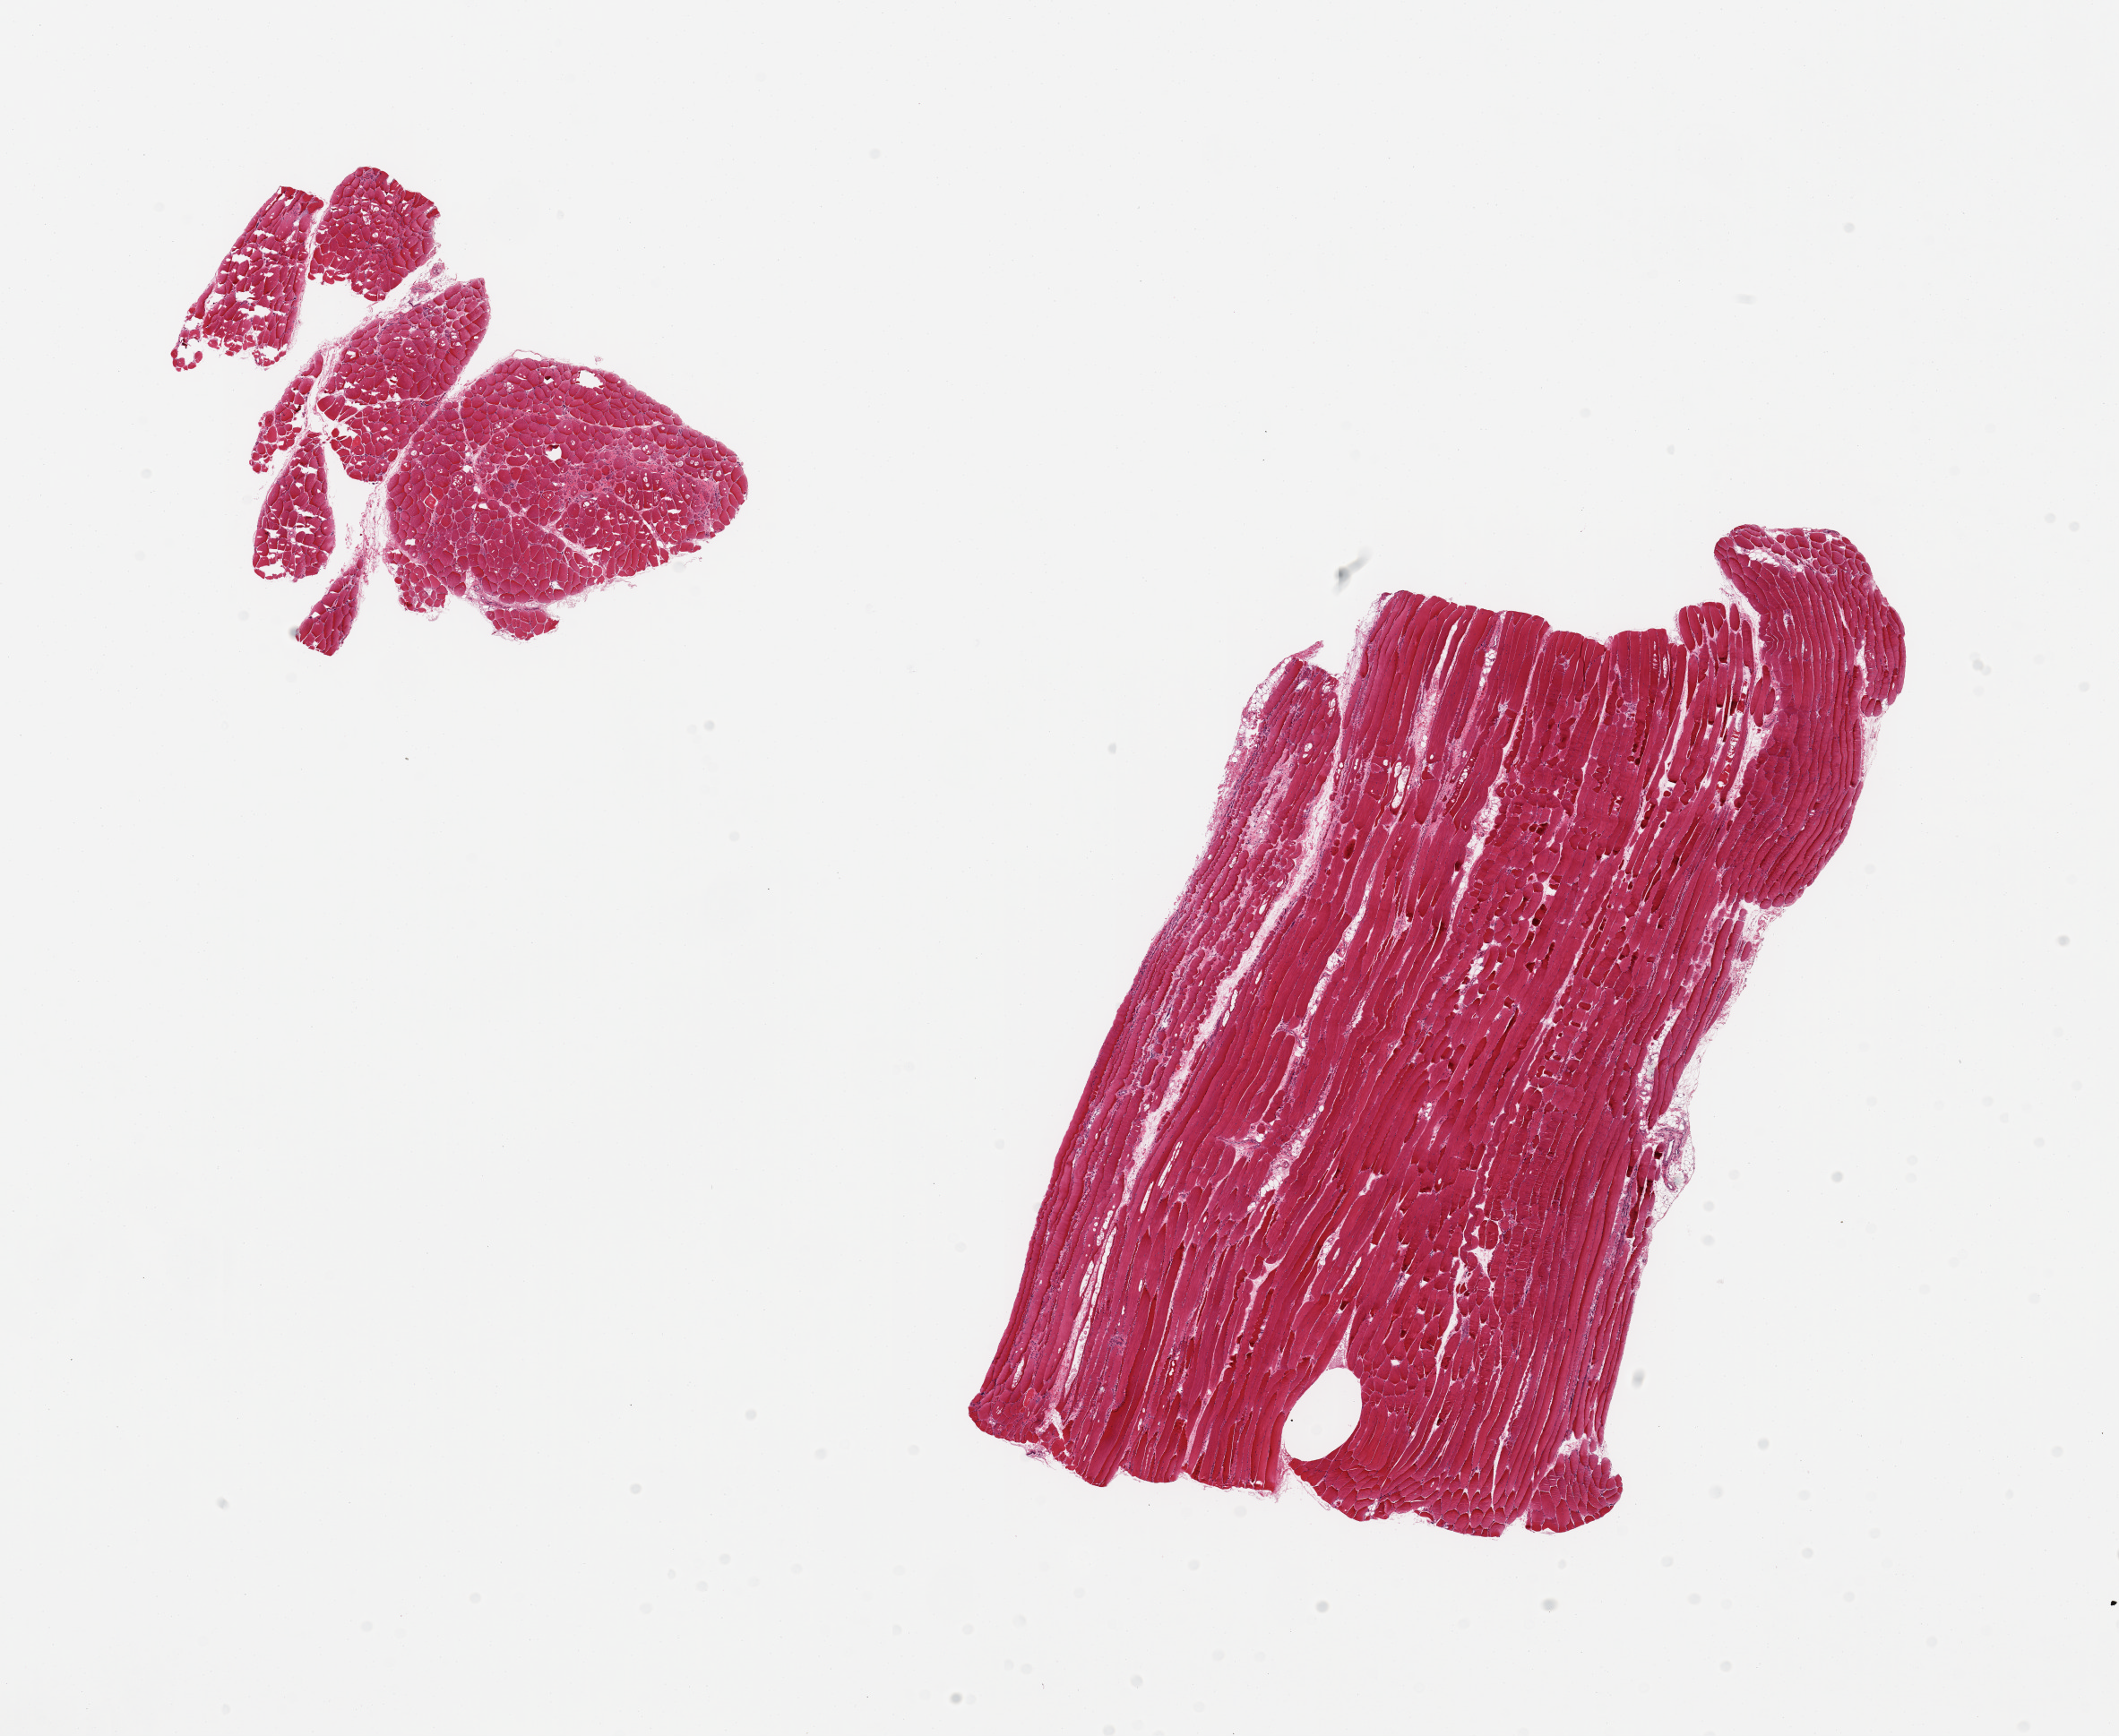
Digitized haematoxylin and eosin-stained section — low-resolution overview of the scanned area, about 18.7 x 15.3 mm, PAXgene-fixed, paraffin-embedded tissue, section of skeletal muscle (target tissue), tissue donor sample. Male donor.
Review note (as recorded): 2 pieces, only trace interstitial fat.